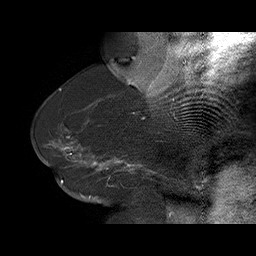
Breast MRI (dynamic contrast-enhanced), one sagittal slice; dynamic contrast-enhanced series, time point 2 of 6 at this slice position (early post-contrast); 1.5 T; TE 4.5 ms, TR 32.4 ms; 3 mm slice thickness; 256 × 256 image matrix, field of view 180 × 180 mm. Female patient. Case-level facts recorded for this patient, not image findings: setting: breast cancer imaged before/during neoadjuvant chemotherapy; receptor status: HR-positive, HER2-negative.
Annotated regions visible in this slice (semi-automatically segmented with operator editing):
- analysis volume of interest (the breast-tissue region the enhancement analysis was run in; not a lesion): bounding box (x1, y1, x2, y2) in pixels: (58, 134, 166, 191)
- tumour enhancement mask (voxels above the 100 % enhancement threshold inside the analysis volume of interest): (60, 142, 150, 172)